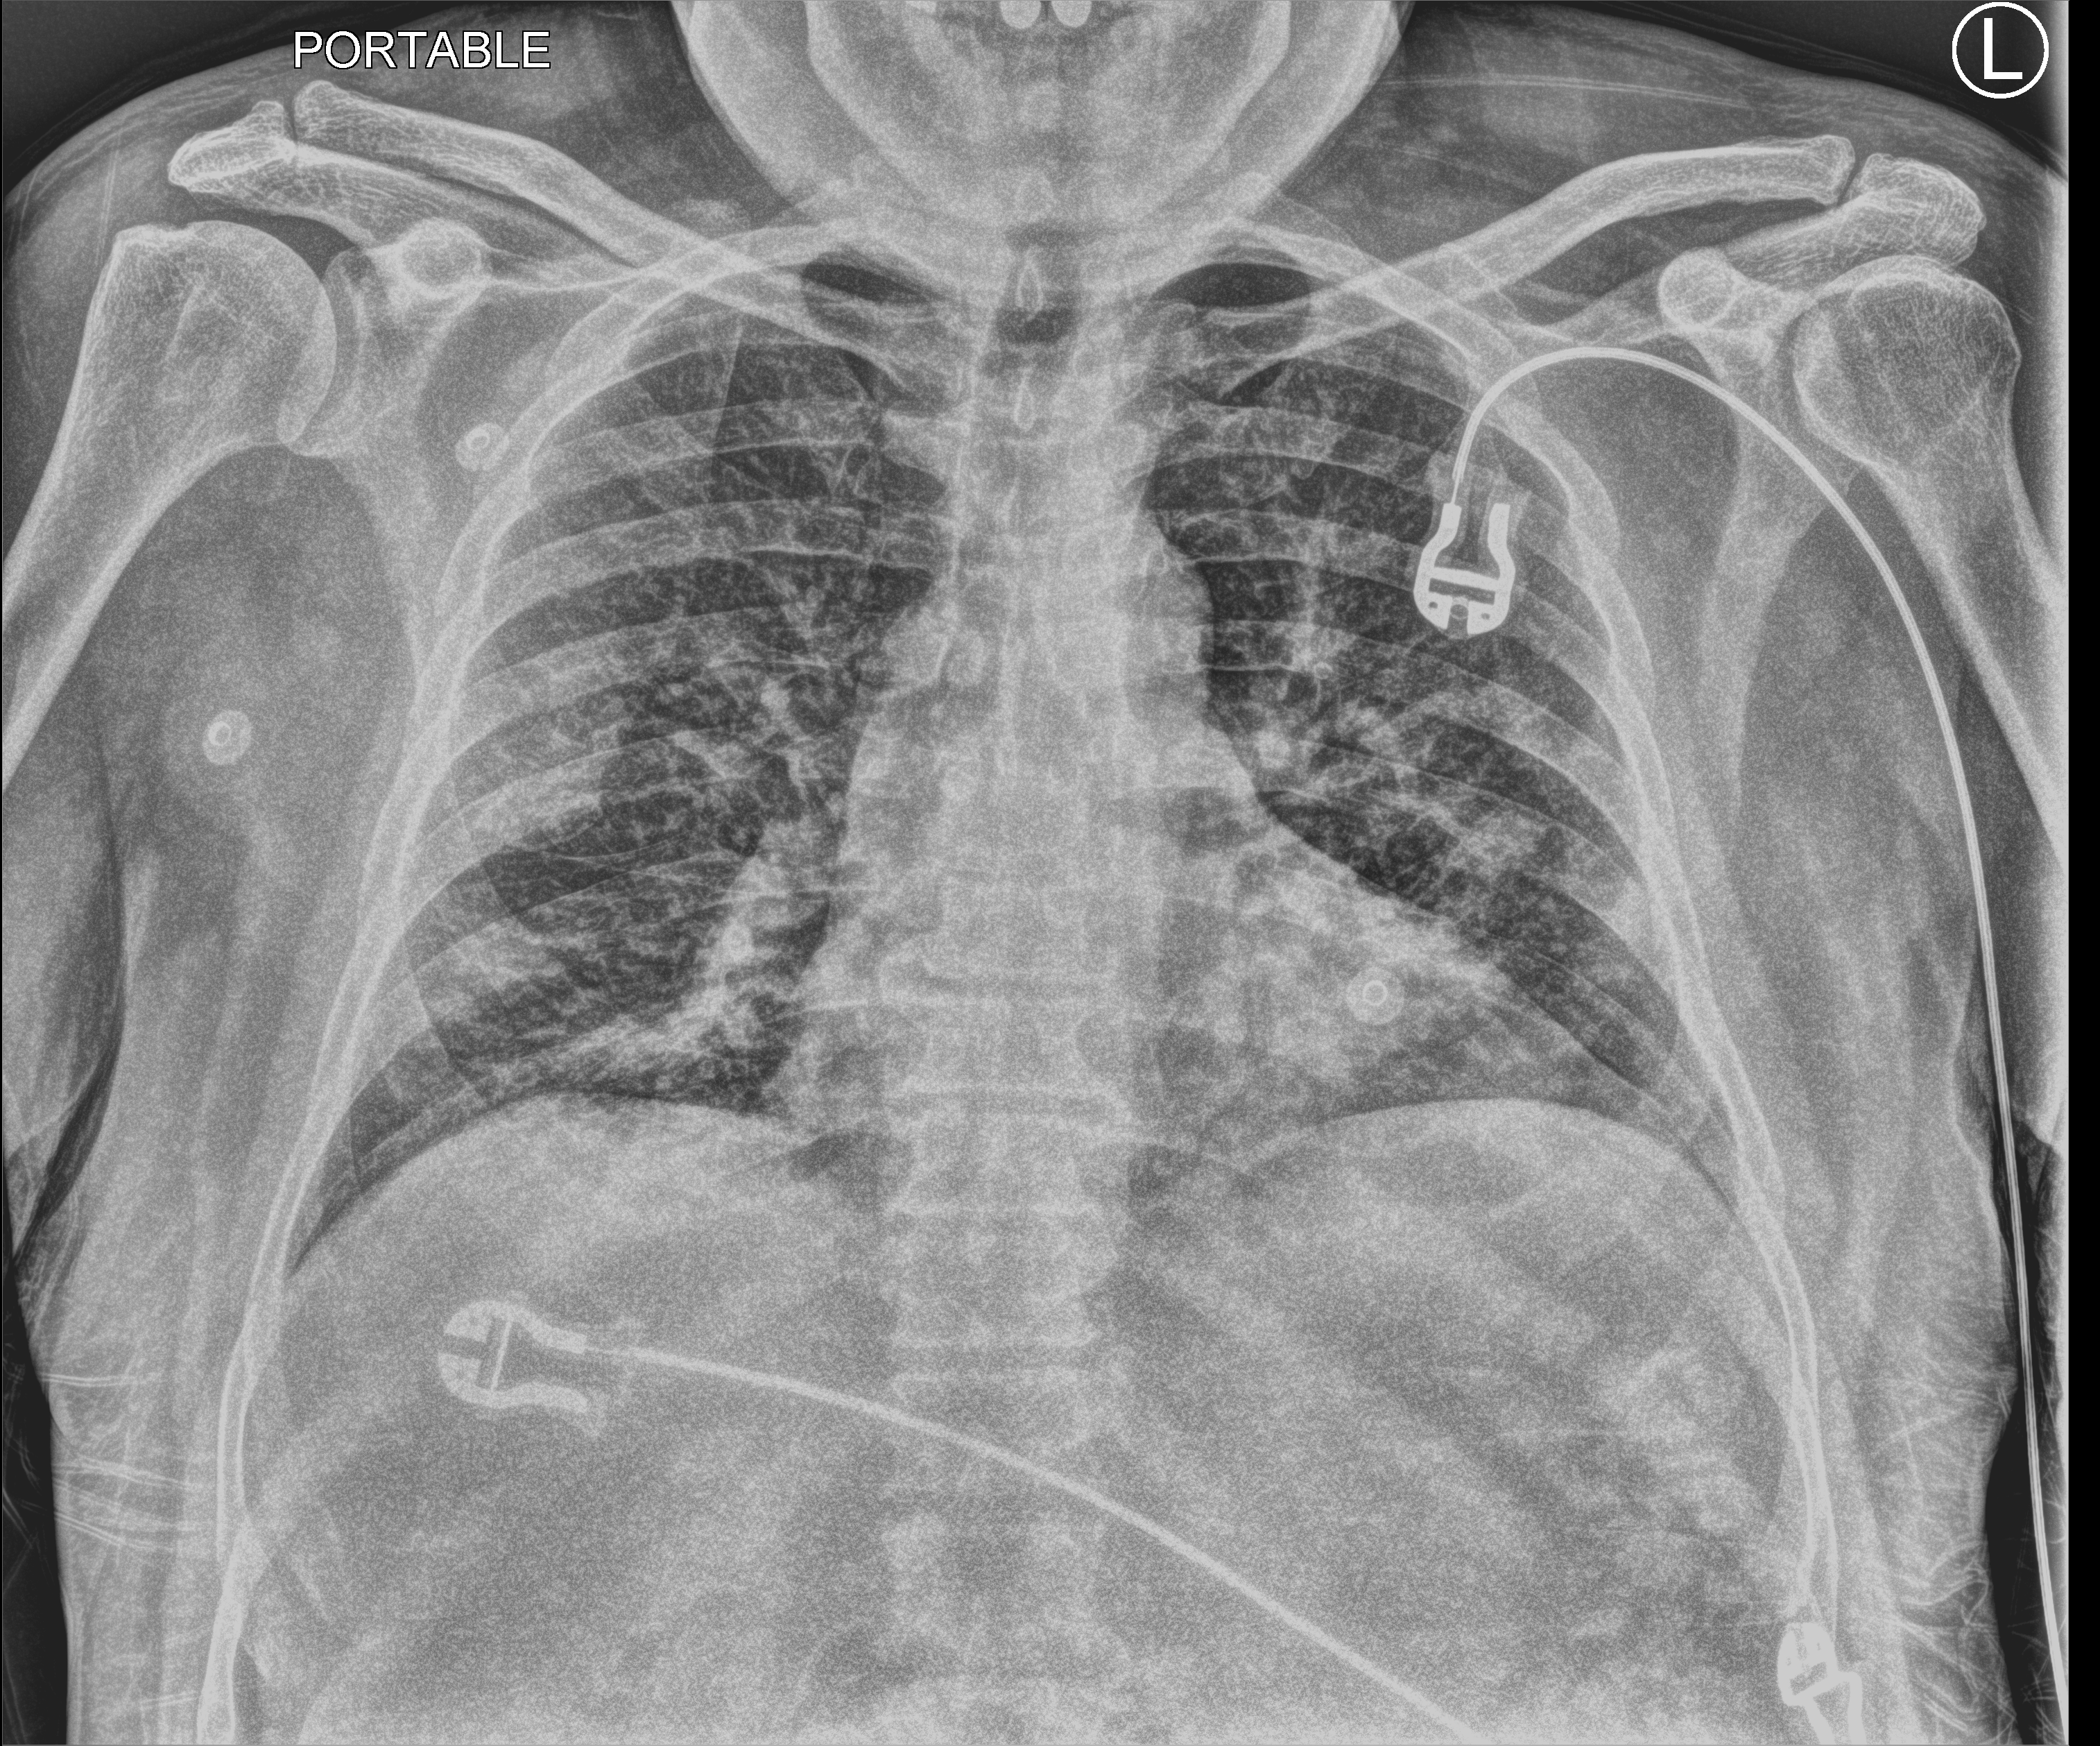
Bedside chest radiograph (computed radiography), anteroposterior (AP) projection. Patient hospitalised with COVID-19; male, aged 18–59 years.
Admission-level facts for this patient (not findings on this image; timing relative to this image not recorded):
- mechanically ventilated during this hospital stay: yes
- other chronic lung disease (admission record): no
- admitted to intensive care during this hospital stay: yes